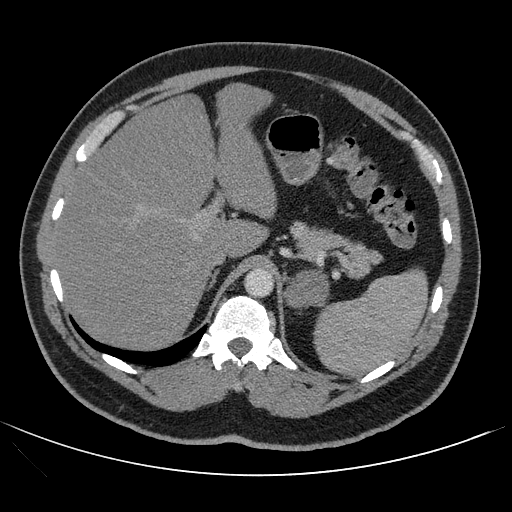
Contrast-enhanced abdominal CT, one axial slice; position 79 of 121 along the scan axis; 120 kVp; intravenous contrast given; soft-tissue window (W 400 / L 40 HU); 2.5 mm slice thickness; 512 × 512 image matrix, field of view 399 × 399 mm. Male patient, age 53 years. From the clinical record (not read from this slice): diagnosis: adrenocortical carcinoma; tumour side: left adrenal; tumour size at pathology: 7.9 cm; Ki-67 index: 20 %; stage (as recorded): 2.
Outlined on this slice (semi-automatically segmented with operator editing):
- mass: bounding box [x1, y1, x2, y2] px = [285, 270, 327, 309]